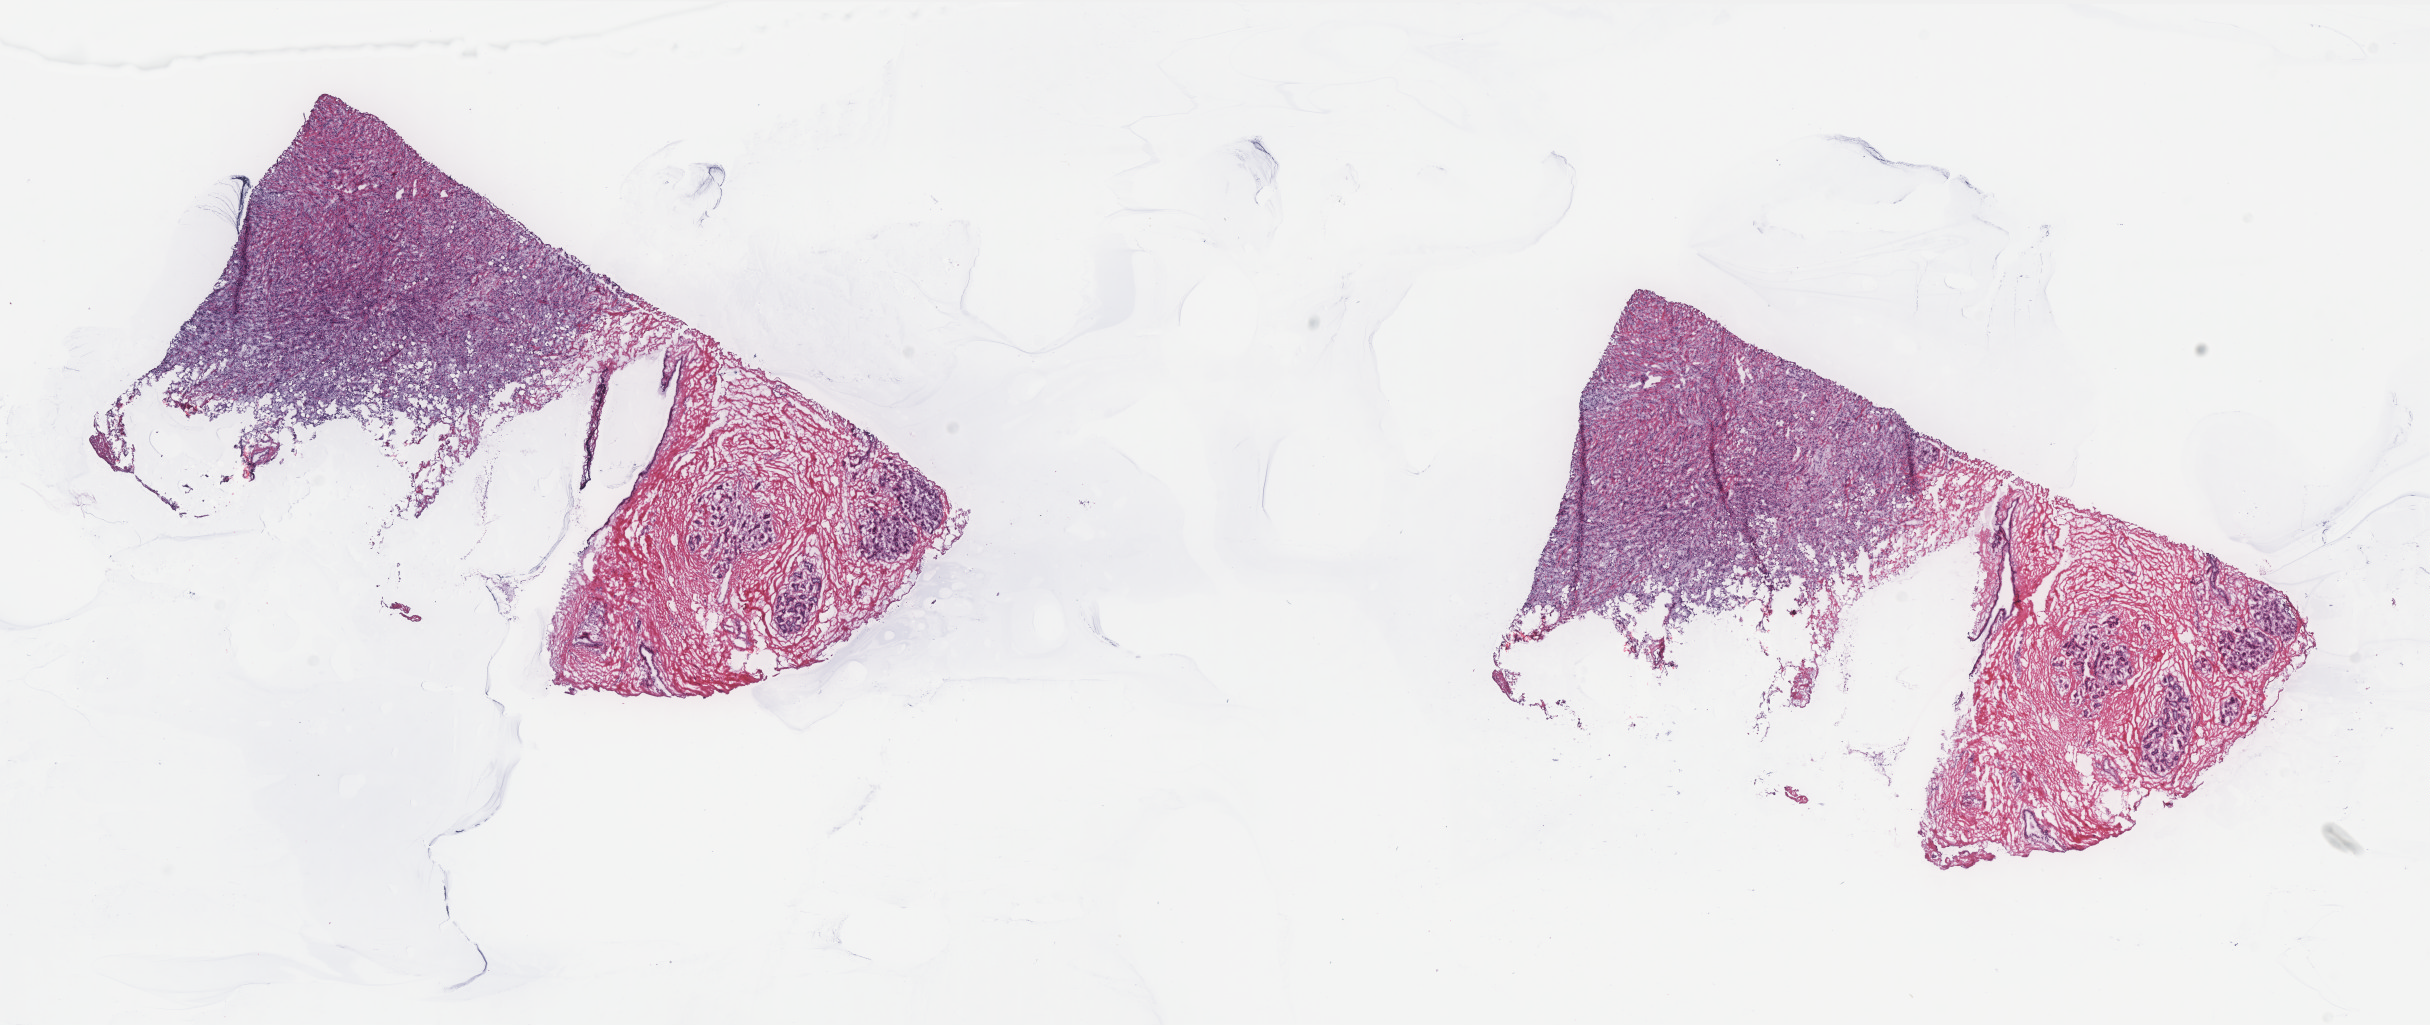
Whole-slide histology image, H&E-stained — whole scanned area (about 19.5 x 8.2 mm, from a 40x scan) shown as a low-resolution overview. Frozen section from the top of the tissue portion. Primary tumour sample from the breast. Female, age 46 years at initial diagnosis. Pathologist review of this section (percent, as recorded): tumour cells 70%, tumour nuclei 70%, normal cells 10%, stromal cells 20%, necrosis 0%. Infiltration values recorded for this section: lymphocyte infiltration 2%, monocyte infiltration 1%, neutrophil infiltration 1%.
• lymph nodes positive (case pathology): 0 of 19 examined
• AJCC pathologic stage: IIB
• diagnosis: Lobular carcinoma, NOS